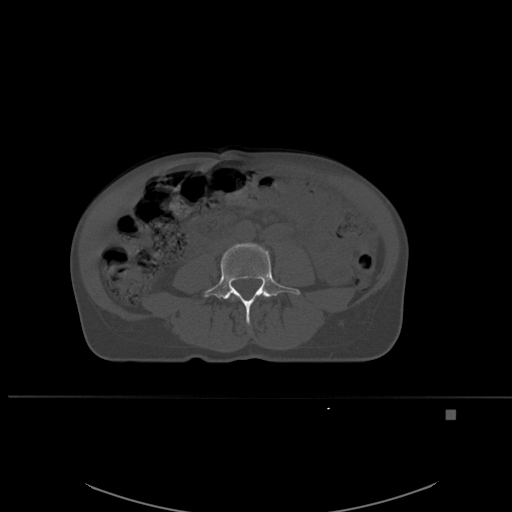
CT including the spine, one axial slice; position 195 of 537 along the scan axis; bone window (W 1800 / L 400 HU); 512 × 512 image matrix, field of view 440 × 440 mm. Female patient, age 45 years. From the clinical record (not read from this slice): primary cancer: lung.
Annotated regions visible in this slice (semi-automatically segmented with operator editing):
- L3 vertebra: box from (x=228, y=293) to (x=267, y=301) px
- L4 vertebra: (x=203, y=242)–(x=300, y=324)